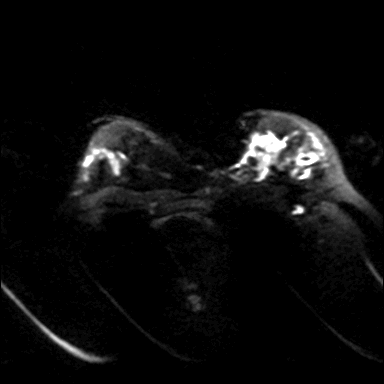
Breast MRI, one axial slice; slice 29 of 36 in the series (ordered by position); diffusion-weighted series; image 2 of 4 stored at this slice position (different b-values; order by instance number); 3 T; 4 mm slice thickness; 384 × 384 image matrix, field of view 320 × 320 mm. Female patient.
Annotated regions visible in this slice (outlined manually by an expert reader):
- tumour on diffusion-weighted imaging: bounding box (x1, y1, x2, y2) in pixels: (295, 156, 314, 163)